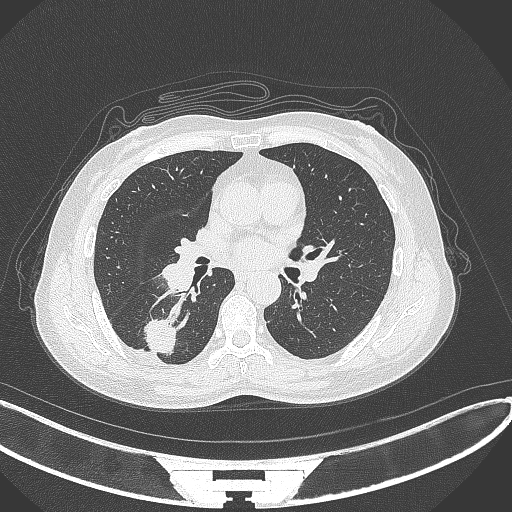
Chest CT, one axial slice; position 160 of 352 along the scan axis; reconstruction kernel B70f; lung window (W 1500 / L -600 HU); 1 mm slice thickness; 512 × 512 image matrix, field of view 400 × 400 mm. Patient: female, 55 years. From the clinical record (not read from this slice): clinical TNM (as recorded): T1c N1 M0.
Annotated regions visible in this slice (bounding box drawn by a radiologist):
- lung tumour (recorded histology: adenocarcinoma): bounding box <140,311,181,360> (left, top, right, bottom; pixels)